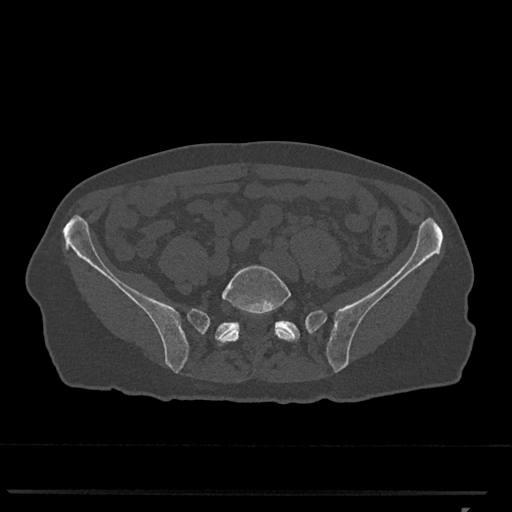
CT including the spine, one axial slice. Position 132 of 793 along the scan axis. Reconstruction kernel Br40s/3. Bone window (W 1800 / L 400 HU). 512 × 512 image matrix, field of view 380 × 380 mm. Female patient, age 62 years. Case-level facts recorded for this patient, not image findings: primary cancer: renal.
Structures marked on this image (semi-automatically segmented with operator editing):
- L5 vertebra: bounding box (x1, y1, x2, y2) in pixels: (217, 265, 298, 346)